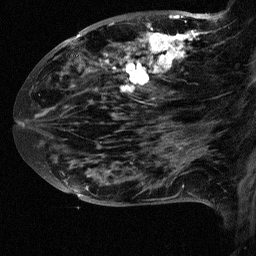
Breast MRI (dynamic contrast-enhanced), one sagittal slice; dynamic contrast-enhanced study with each time point stored as its own series, time point 2 of 3 at this slice position (early post-contrast, ordered by acquisition time); 1.5 T; TE 4.5 ms, TR 11 ms; 2.5 mm slice thickness; 256 × 256 image matrix. Female patient, age 38 years. From the clinical record (not read from this slice): setting: breast cancer imaged before/during neoadjuvant chemotherapy; receptor status: HR-positive, HER2-negative.
Outlined on this slice (semi-automatic segmentation, software-assisted and operator-edited):
- analysis volume of interest (the breast-tissue region the enhancement analysis was run in; not a lesion): bounding box <88,18,252,126> (left, top, right, bottom; pixels)
- tumour enhancement mask (voxels above the 90 % enhancement threshold inside the analysis volume of interest): <119,18,211,99>